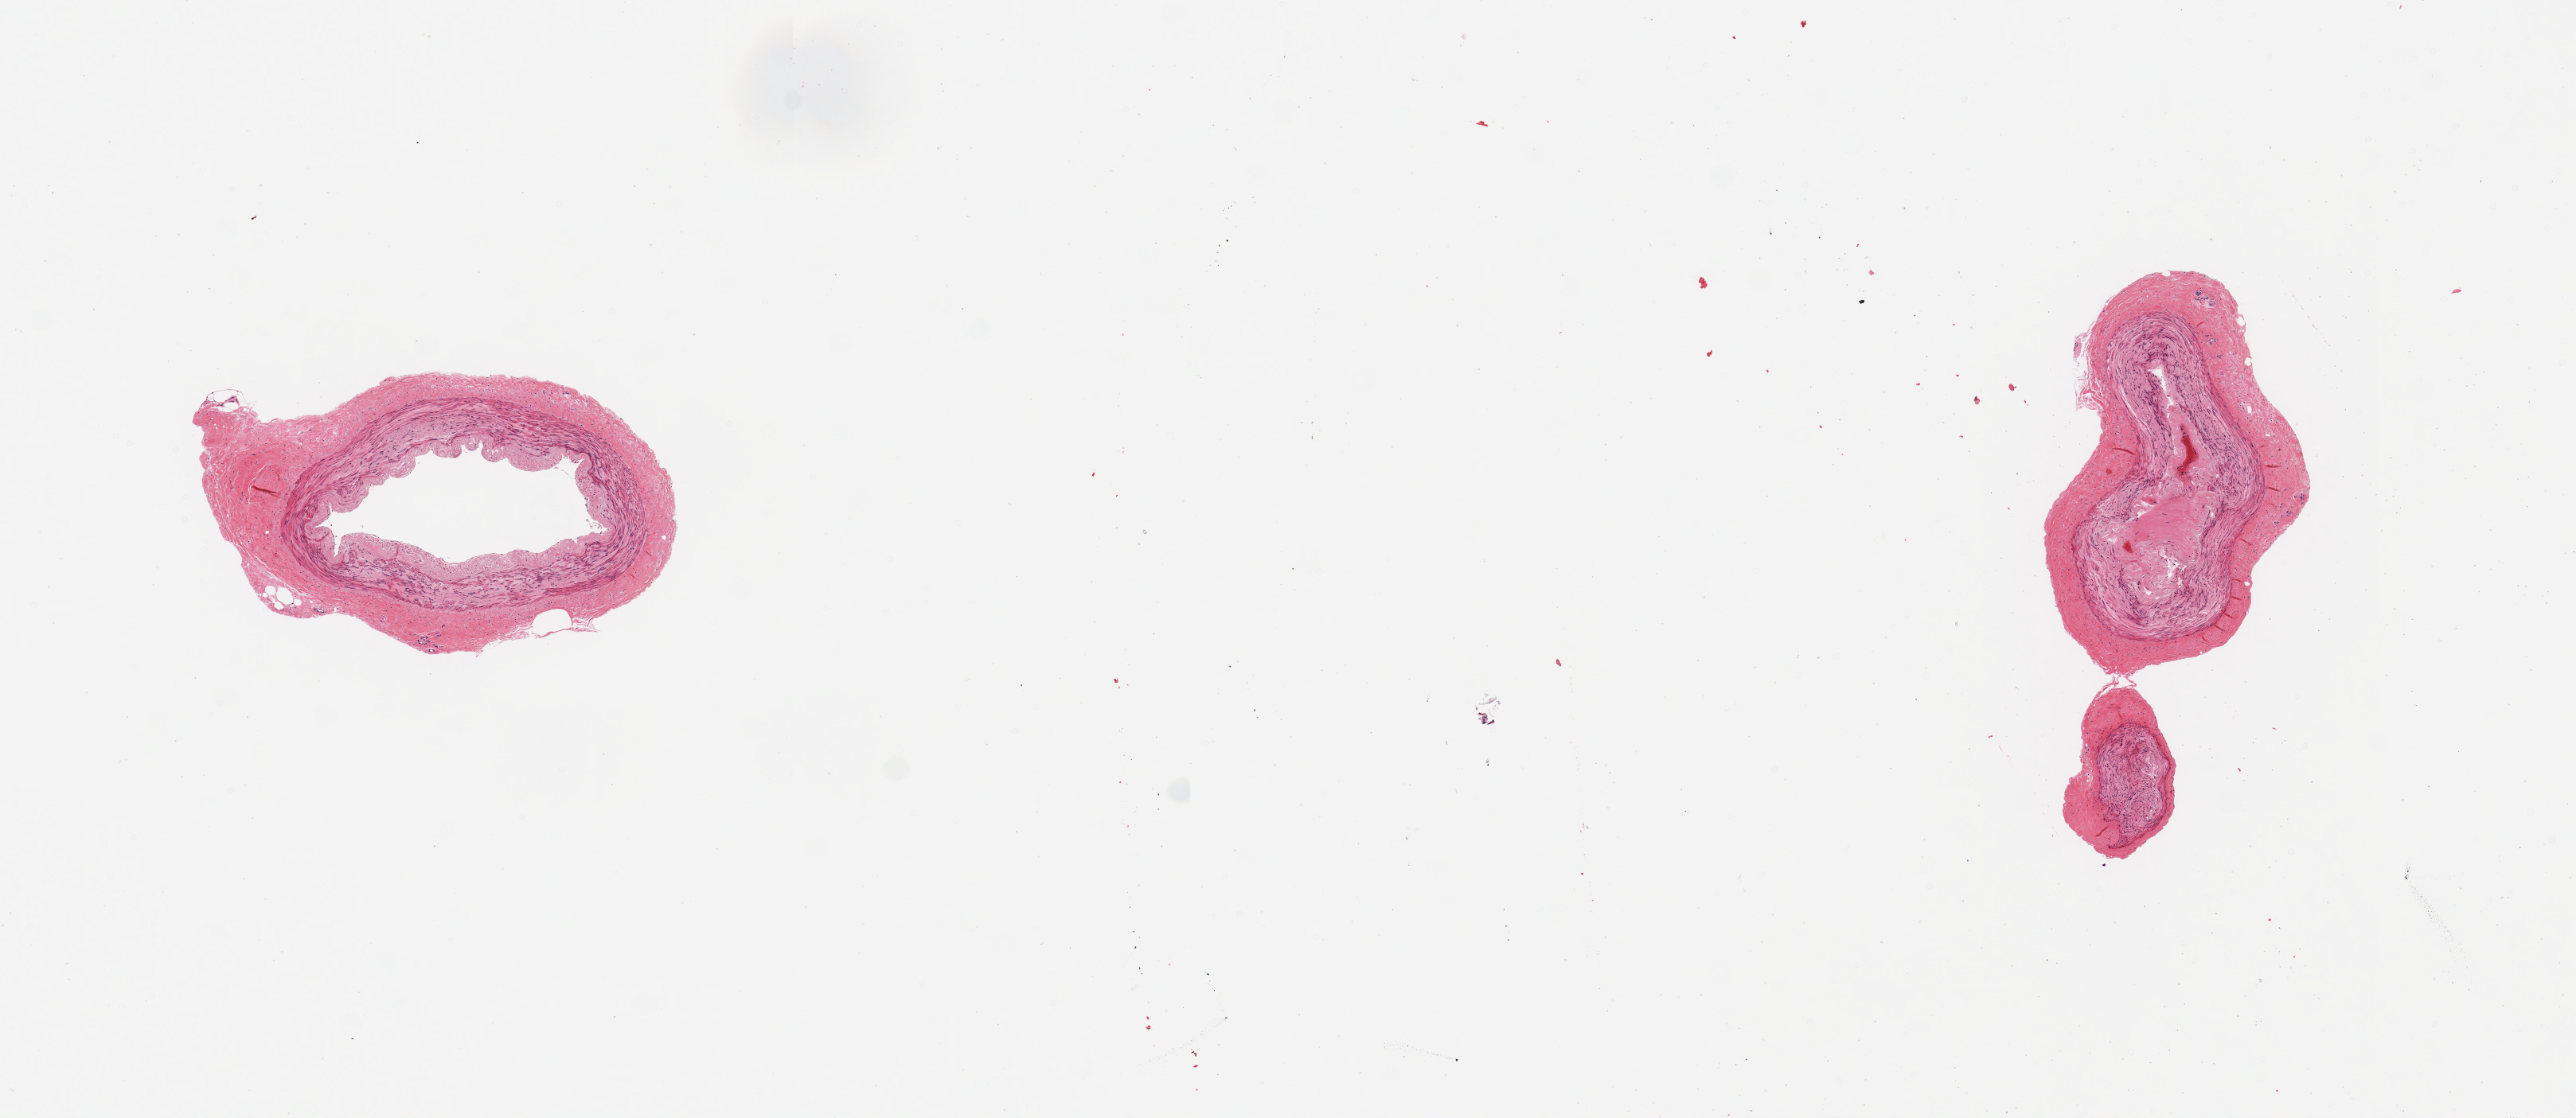
Whole-slide image, H&E stain — shown as a low-resolution overview of the whole scanned area (about 12.8 x 5.6 mm, from a 20x scan), PAXgene-fixed paraffin-embedded (PFPE) section, target tissue: tibial artery, tissue donor sample. Donor: female.
Reviewer comment on this tissue sample: 2 pieces, minimal fat, good specimens.